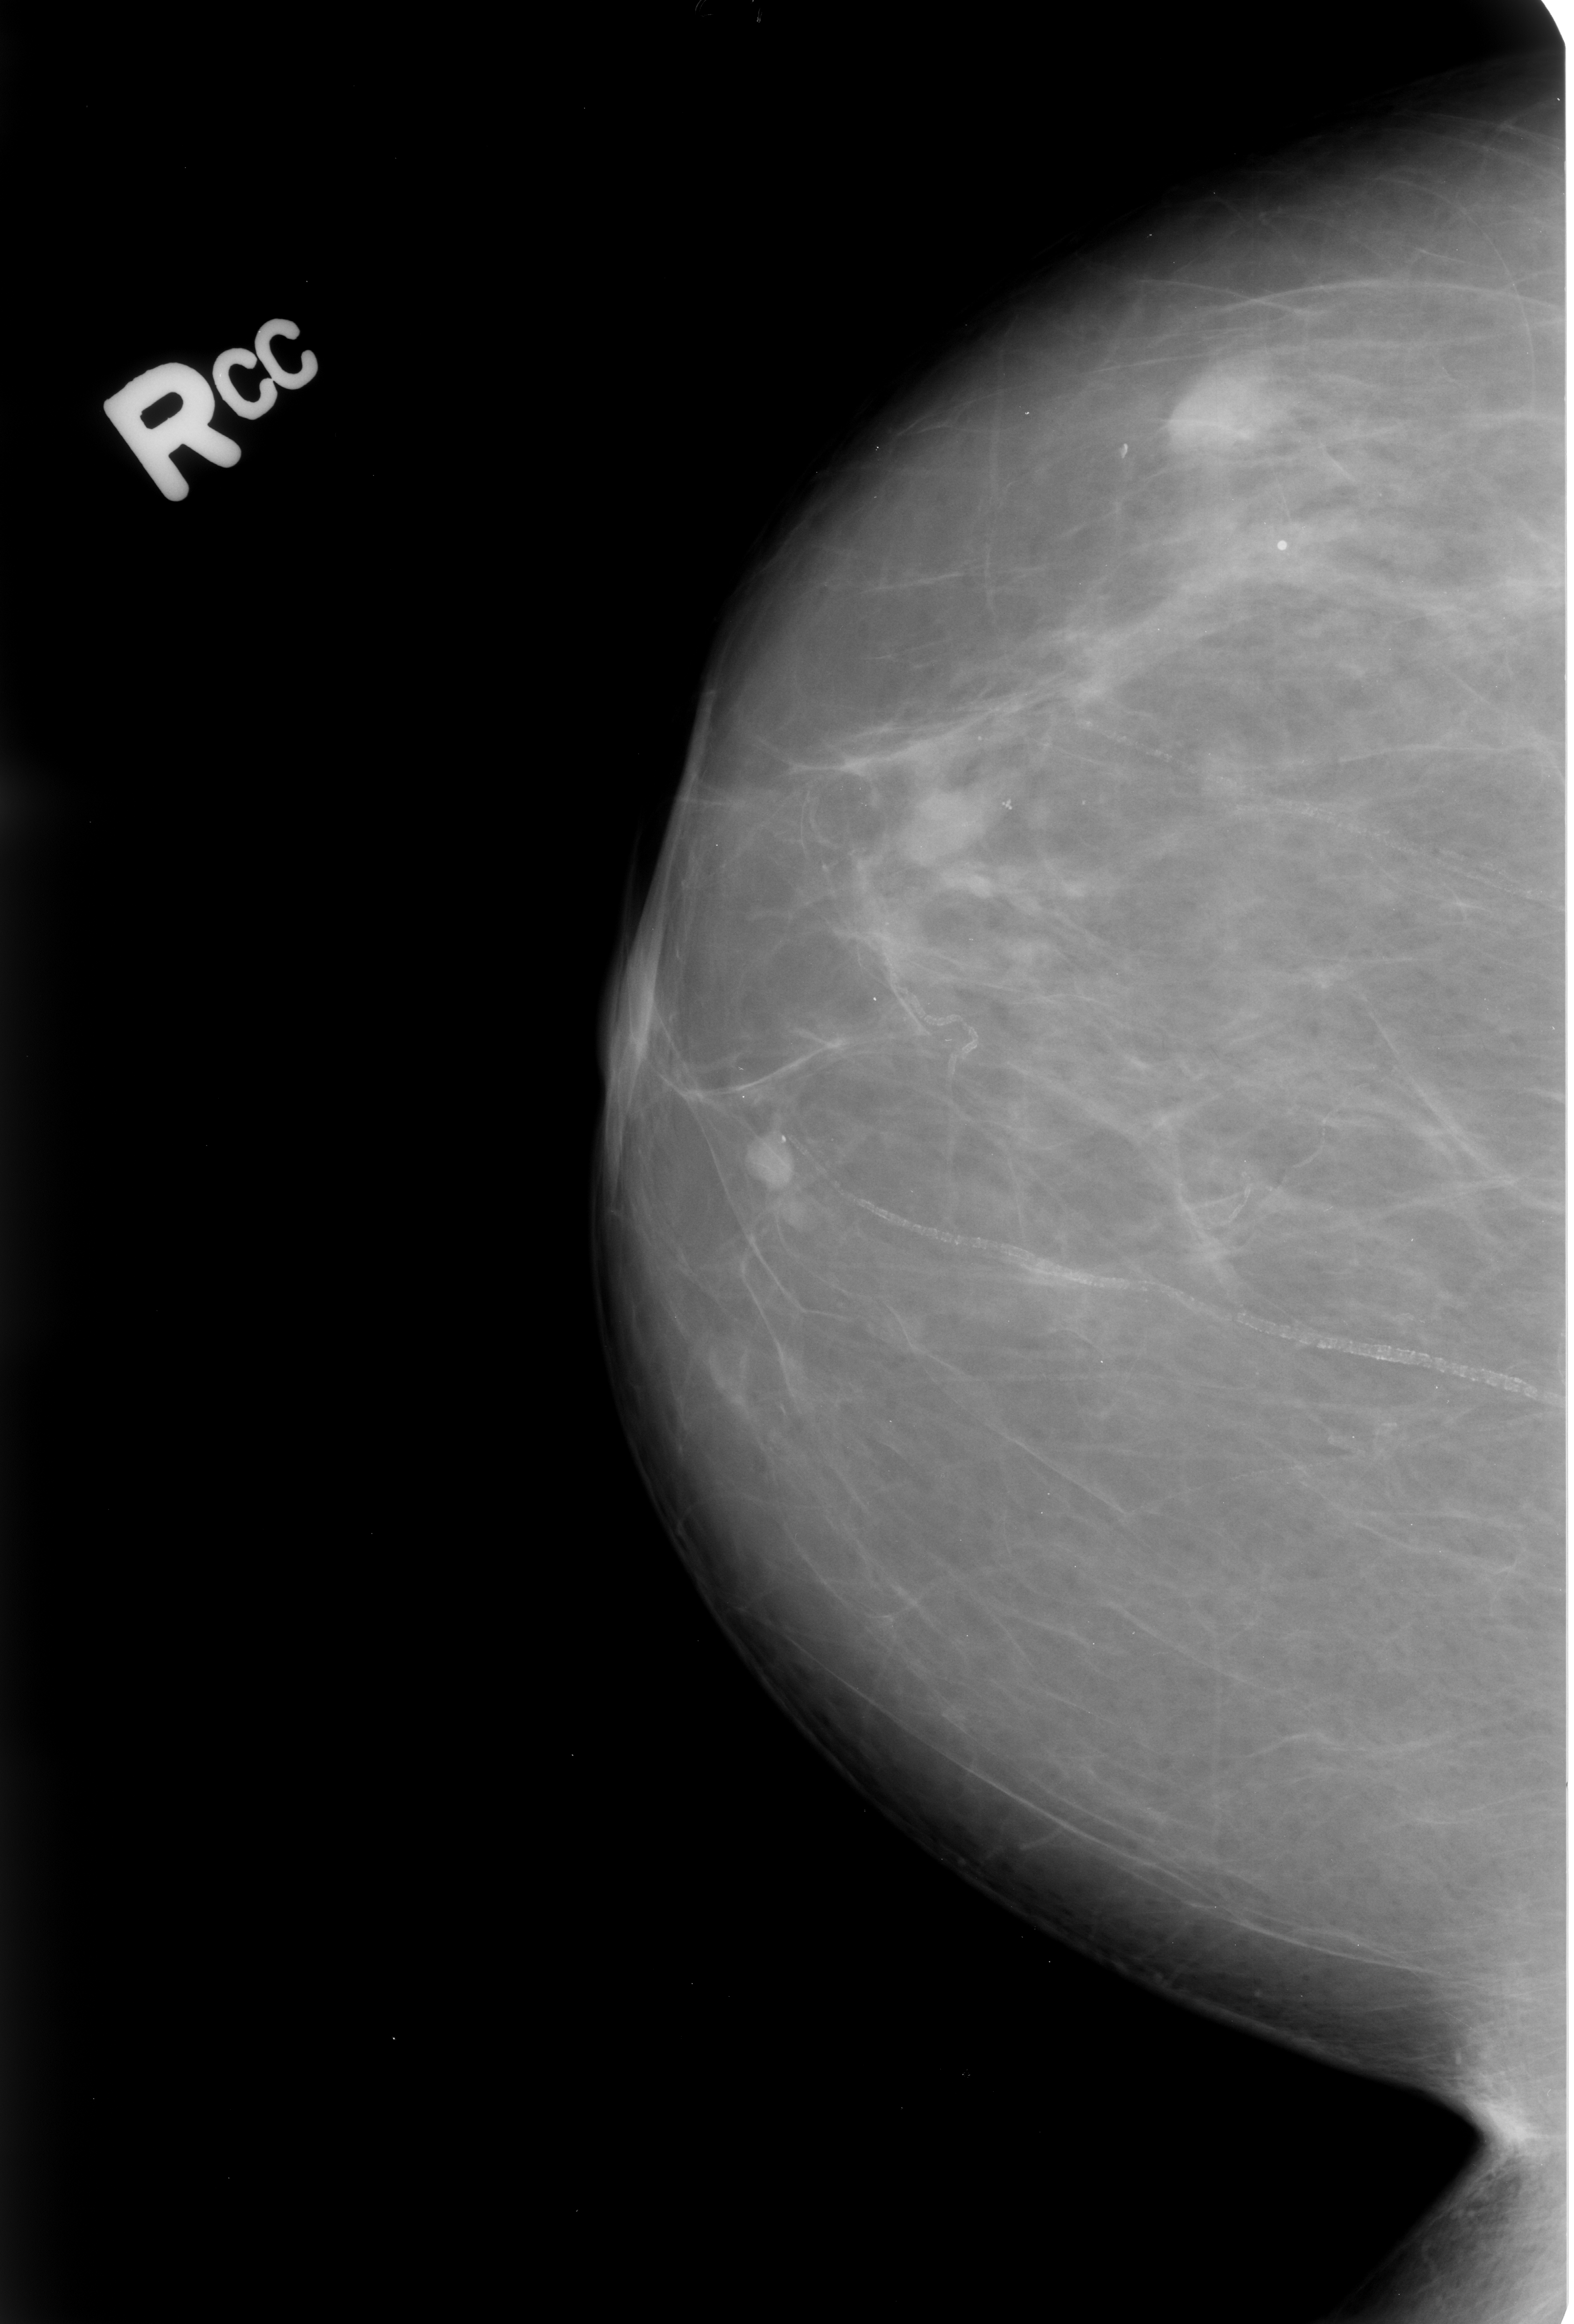
Scanned film-screen mammogram, right breast, CC view, BI-RADS breast density category 2 (scale 1–4).
- Radiologist-marked abnormalities on this image: Finding 1 of 2: calcifications, morphology round and regular; BI-RADS assessment category 2; subtlety rating 4 on a 1 (subtle) to 5 (obvious) scale; benign; no additional work-up was recommended (benign without callback).
- Finding 2 of 2: calcifications, morphology vascular; BI-RADS assessment category 2; subtlety rating 4 on a 1 (subtle) to 5 (obvious) scale; benign without callback (not worked up further).